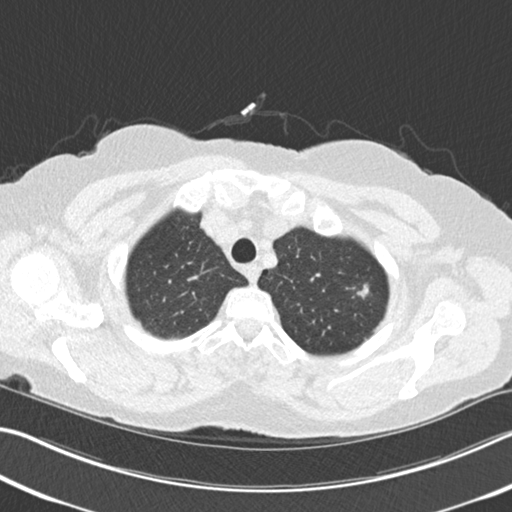
Low-dose screening chest CT, one axial slice; reconstruction kernel B30f; 120 kVp; lung window (W 1500 / L -600 HU); 2 mm slice thickness; 512 × 512 image matrix.
Annotated regions visible in this slice (expert manual segmentation):
- lesion 1 (tumor): box from (x=357, y=284) to (x=369, y=298) px